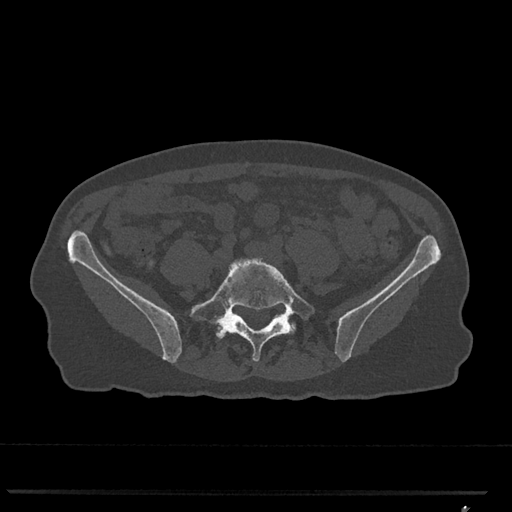
CT including the spine, one axial slice; position 151 of 793 along the scan axis; reconstruction kernel Br40s/3; 120 kVp; bone window (W 1800 / L 400 HU); 0.5 mm slice thickness; 512 × 512 image matrix, field of view 380 × 380 mm. Patient: female, 62 years. Case-level facts recorded for this patient, not image findings: primary cancer: renal.
Structures marked on this image (semi-automatically segmented with operator editing):
- L5 vertebra: bounding box [x1, y1, x2, y2] px = [190, 258, 315, 362]